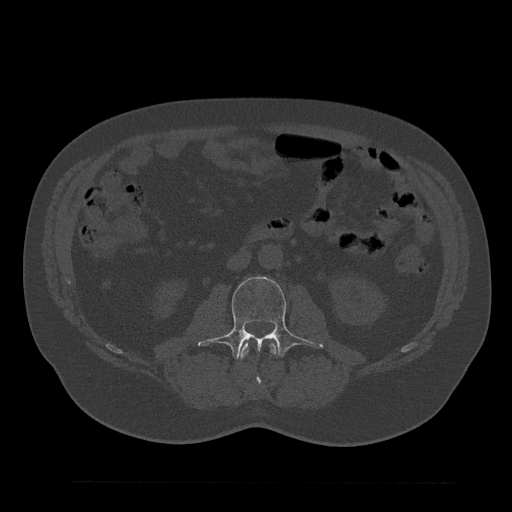
CT including the spine, one axial slice; slice 48 of 797 in the series (ordered by position); reconstruction kernel Br40s/3; 120 kVp; bone window (W 1800 / L 400 HU); 0.5 mm slice thickness; 512 × 512 image matrix. Male patient, age 61 years. From the clinical record (not read from this slice): primary cancer: prostate.
Structures marked on this image (semi-automatic segmentation, software-assisted and operator-edited):
- L2 vertebra: bounding box <239,343,277,386> (left, top, right, bottom; pixels)
- L3 vertebra: <198,277,323,359>